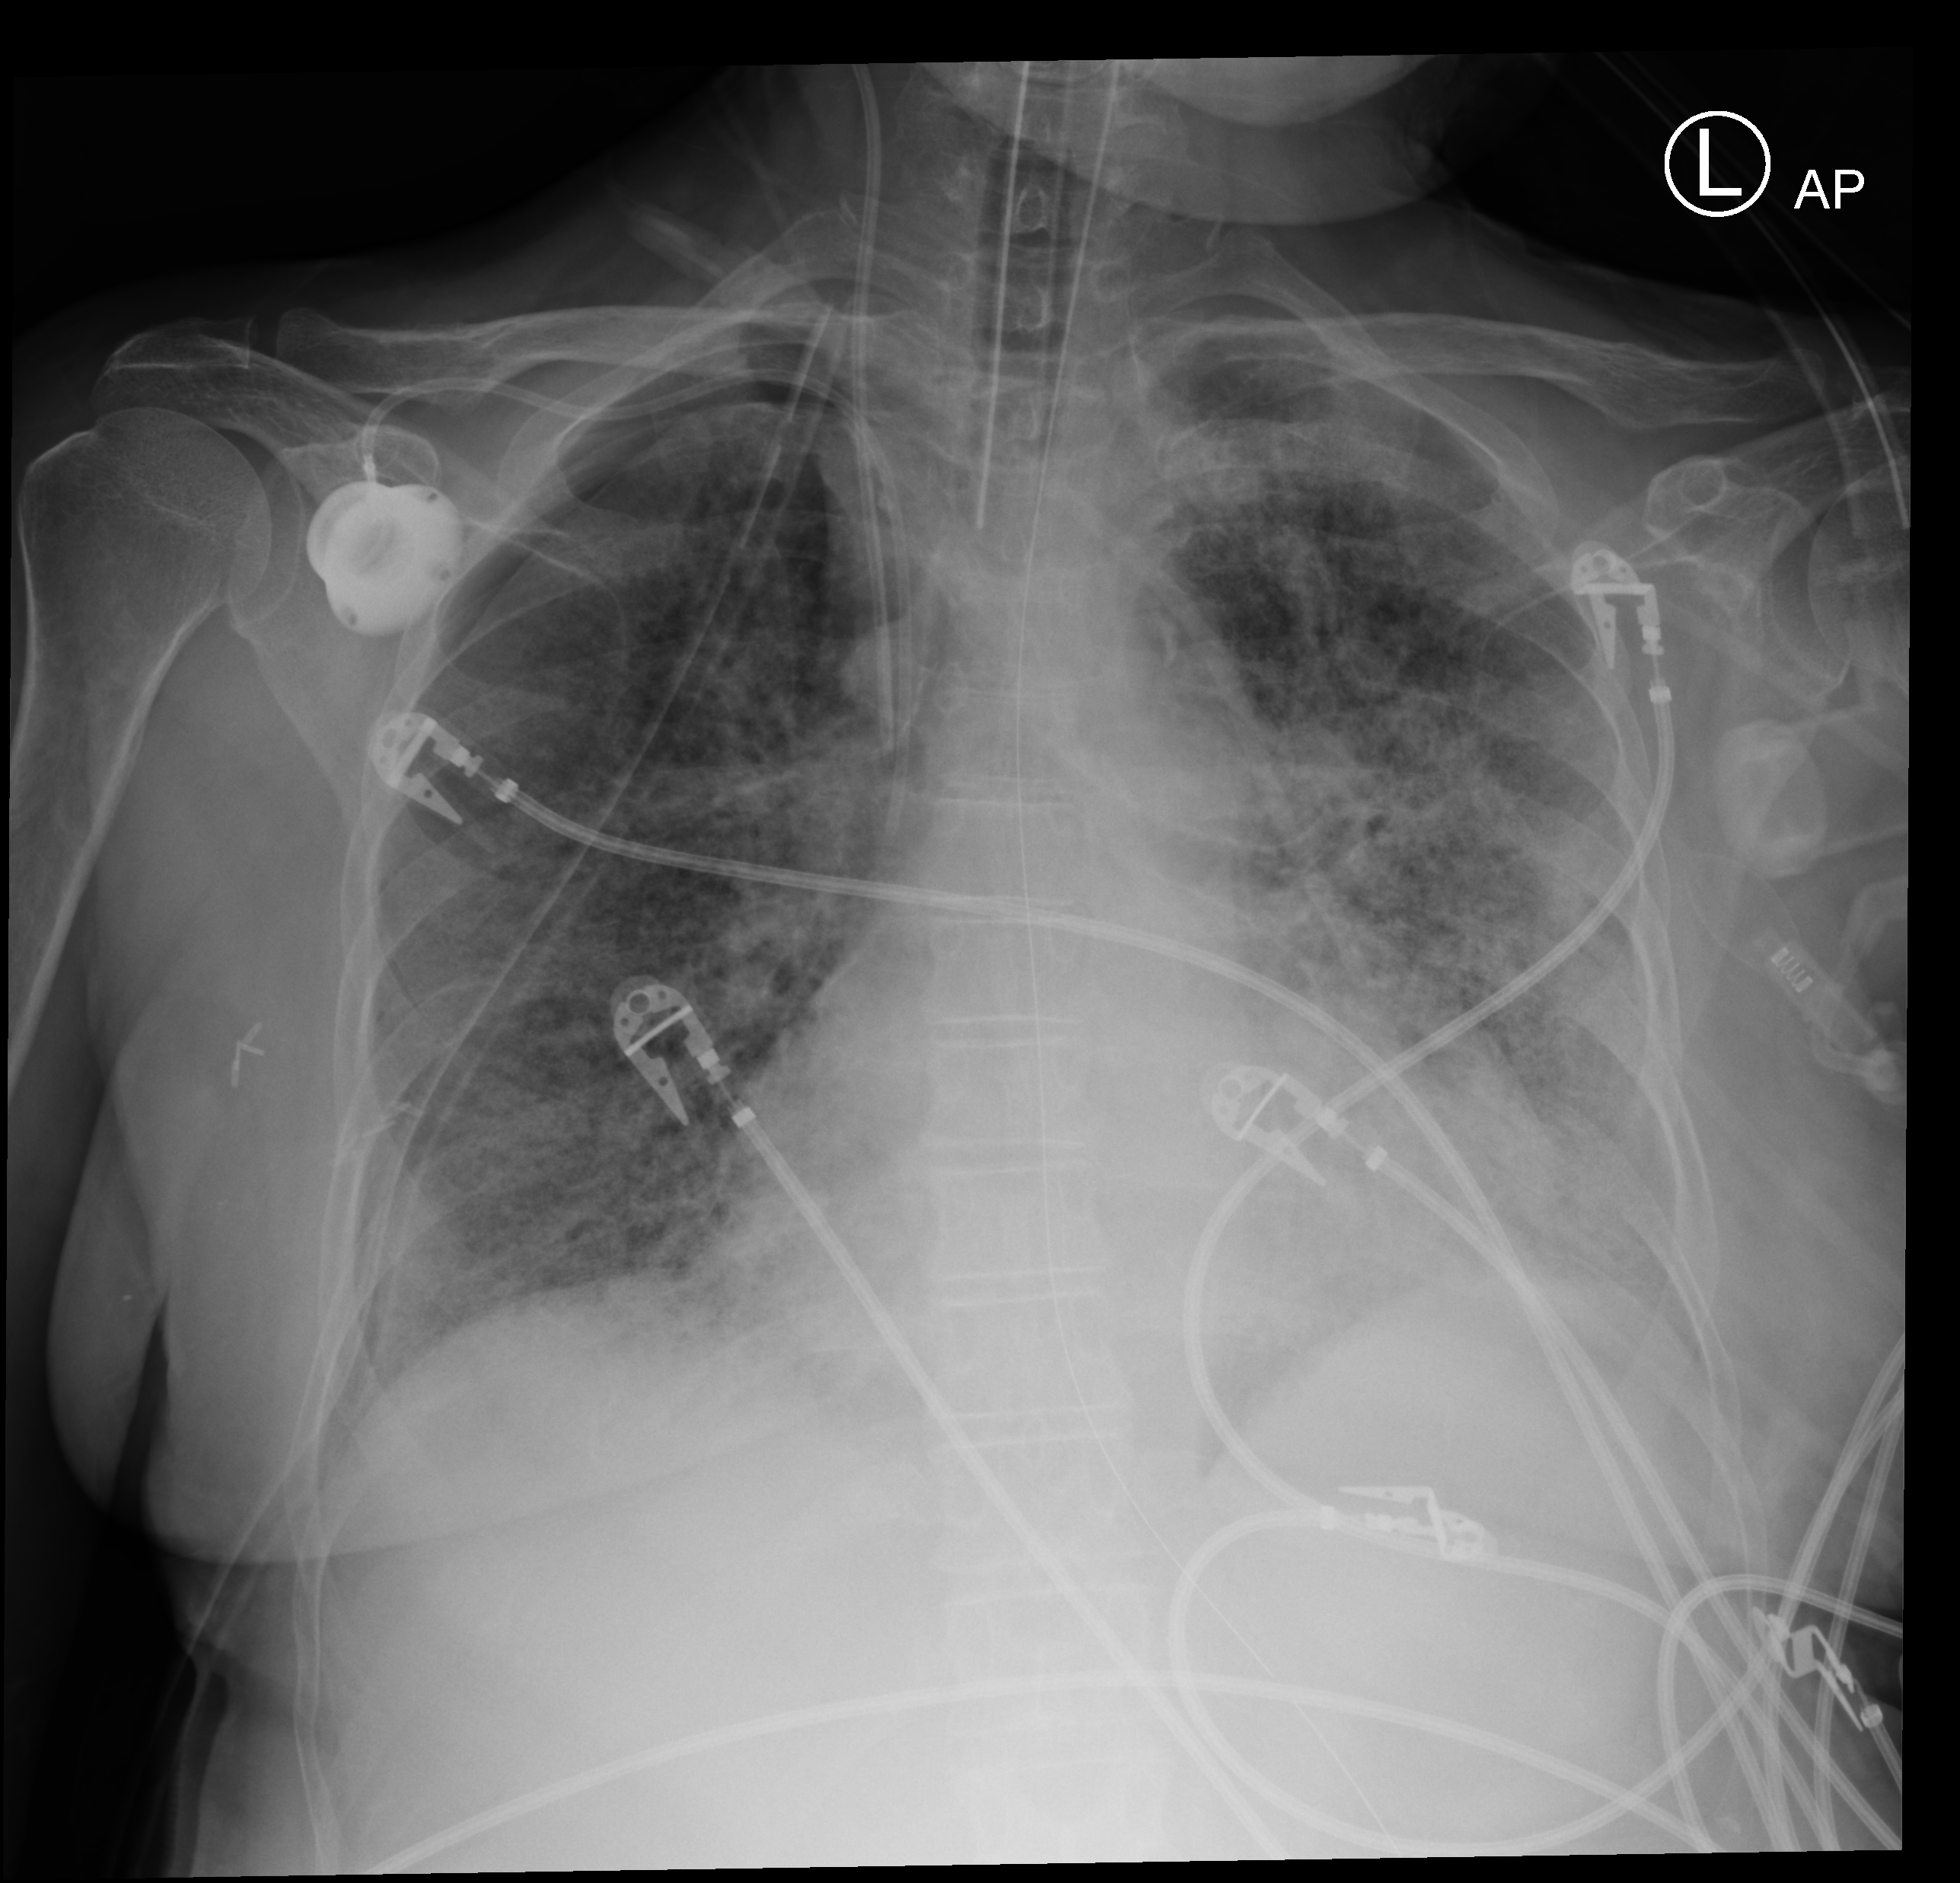
Chest X-ray (portable), anteroposterior (AP) projection. Patient hospitalised with COVID-19; female, aged 60–74 years.
From the hospital-stay record, not from the radiograph (when in the stay this image was taken is not recorded):
- admitted to intensive care during this hospital stay: yes